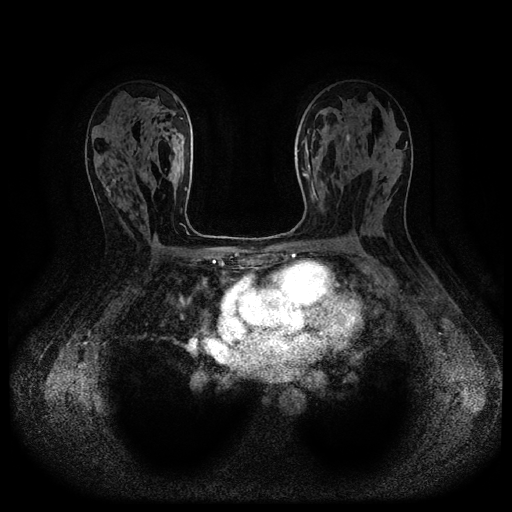
Breast MRI (dynamic contrast-enhanced, multi-phase), one axial slice; slice 64 of 116 in the series (ordered by position); dynamic contrast-enhanced series, time point 2 of 5 at this slice position (early post-contrast); 1.5 T; TE 2.6 ms, TR 5.3 ms; 2.2 mm slice thickness; 512 × 512 image matrix, field of view 340 × 340 mm. Patient: female, 54 years.
Outlined on this slice (semi-automatic segmentation, software-assisted and operator-edited):
- breast lesion (labelled benign in the annotation): bounding box (x1, y1, x2, y2) in pixels: (345, 133, 350, 145)